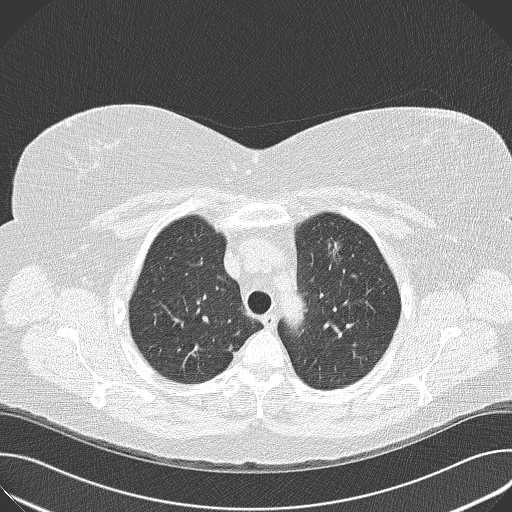
Axial slice from a low-dose chest CT screening exam, baseline screening round, lung window (W 1500 / L -600 HU), 120 kVp, slice 114 of 143 in the series, 512 × 512 image matrix, field of view 380 × 380 mm. Female participant, aged 57 years at enrolment. Current smoker at enrolment.
Expert-annotated lung lesion, bounding box (x1, y1, x2, y2) in pixels: (317, 235, 350, 272). The screening reader recorded 3 non-calcified nodules or masses ≥4 mm on this exam (lingula, right middle lobe, left upper lobe); which of them this box marks is not recorded. Later outcome: lung cancer diagnosed 446 days after this screen (after the second annual screen) — adenocarcinoma, NOS, left upper lobe, poorly differentiated (G3), stage IA (AJCC 6th edition), 24 mm at pathology.